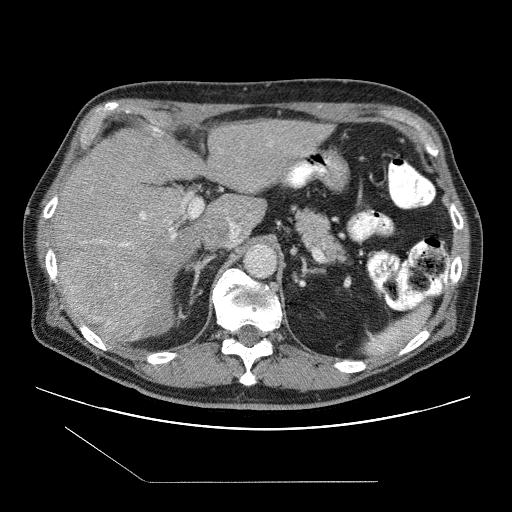
Contrast-enhanced abdominal CT (liver protocol), one axial slice. Slice 61 of 109 in the series (ordered by position). One of 2 acquisitions stored at this slice position. Soft-tissue window (W 400 / L 40 HU). 2.5 mm slice thickness. 512 × 512 image matrix. Case-level facts recorded for this patient, not image findings: diagnosis: hepatocellular carcinoma (patient treated with transarterial chemoembolisation; whether this scan precedes or follows treatment is not stated here); TNM stage (as recorded): Stage-IIIB; Child-Pugh class: A.
Structures marked on this image (semi-automatically segmented with operator editing):
- liver parenchyma outside the tumour (the mass and vessels are separate outlines, so this box may not span the whole liver): bounding box (x1, y1, x2, y2) in pixels: (52, 120, 331, 340)
- mass: (59, 251, 158, 339)
- liver vessels: (105, 198, 238, 246)